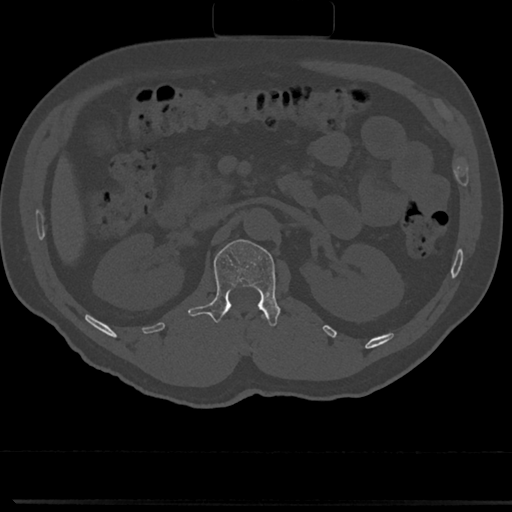
CT including the spine, one axial slice; slice 92 of 817 in the series (ordered by position); 120 kVp; bone window (W 1800 / L 400 HU); 0.5 mm slice thickness; 512 × 512 image matrix, field of view 355 × 355 mm. Patient: male, 61 years. From the clinical record (not read from this slice): primary cancer: prostate.
Annotated regions visible in this slice (semi-automatic segmentation, software-assisted and operator-edited):
- L1 vertebra: box from (x=191, y=239) to (x=282, y=326) px